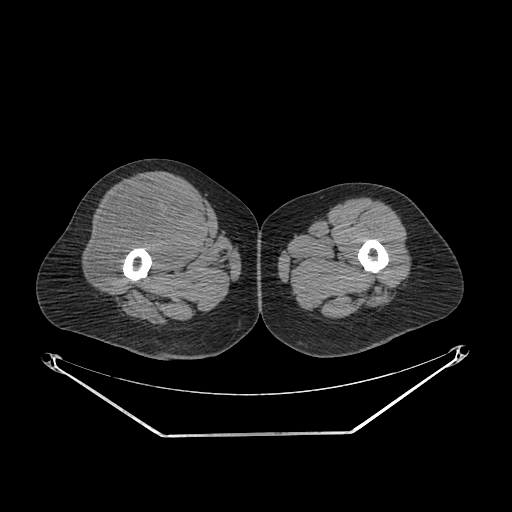
CT of an extremity soft-tissue mass (from a PET/CT study), one axial slice; position 255 of 311 along the scan axis; reconstruction kernel SOFT; soft-tissue window (W 400 / L 40 HU); 3.75 mm slice thickness; 512 × 512 image matrix, field of view 500 × 500 mm. Female patient. From the clinical record (not read from this slice): histological type: pleiomorphic undifferentiated sarcoma; grade: high; site of the primary tumour: right quadricep.
Annotated regions visible in this slice (expert contour drawn on MRI and transferred to this co-registered scan by the dataset authors):
- tumour plus oedema (research contour): bounding box [x1, y1, x2, y2] px = [91, 183, 200, 289]
- tumour (research contour): [91, 183, 200, 289]